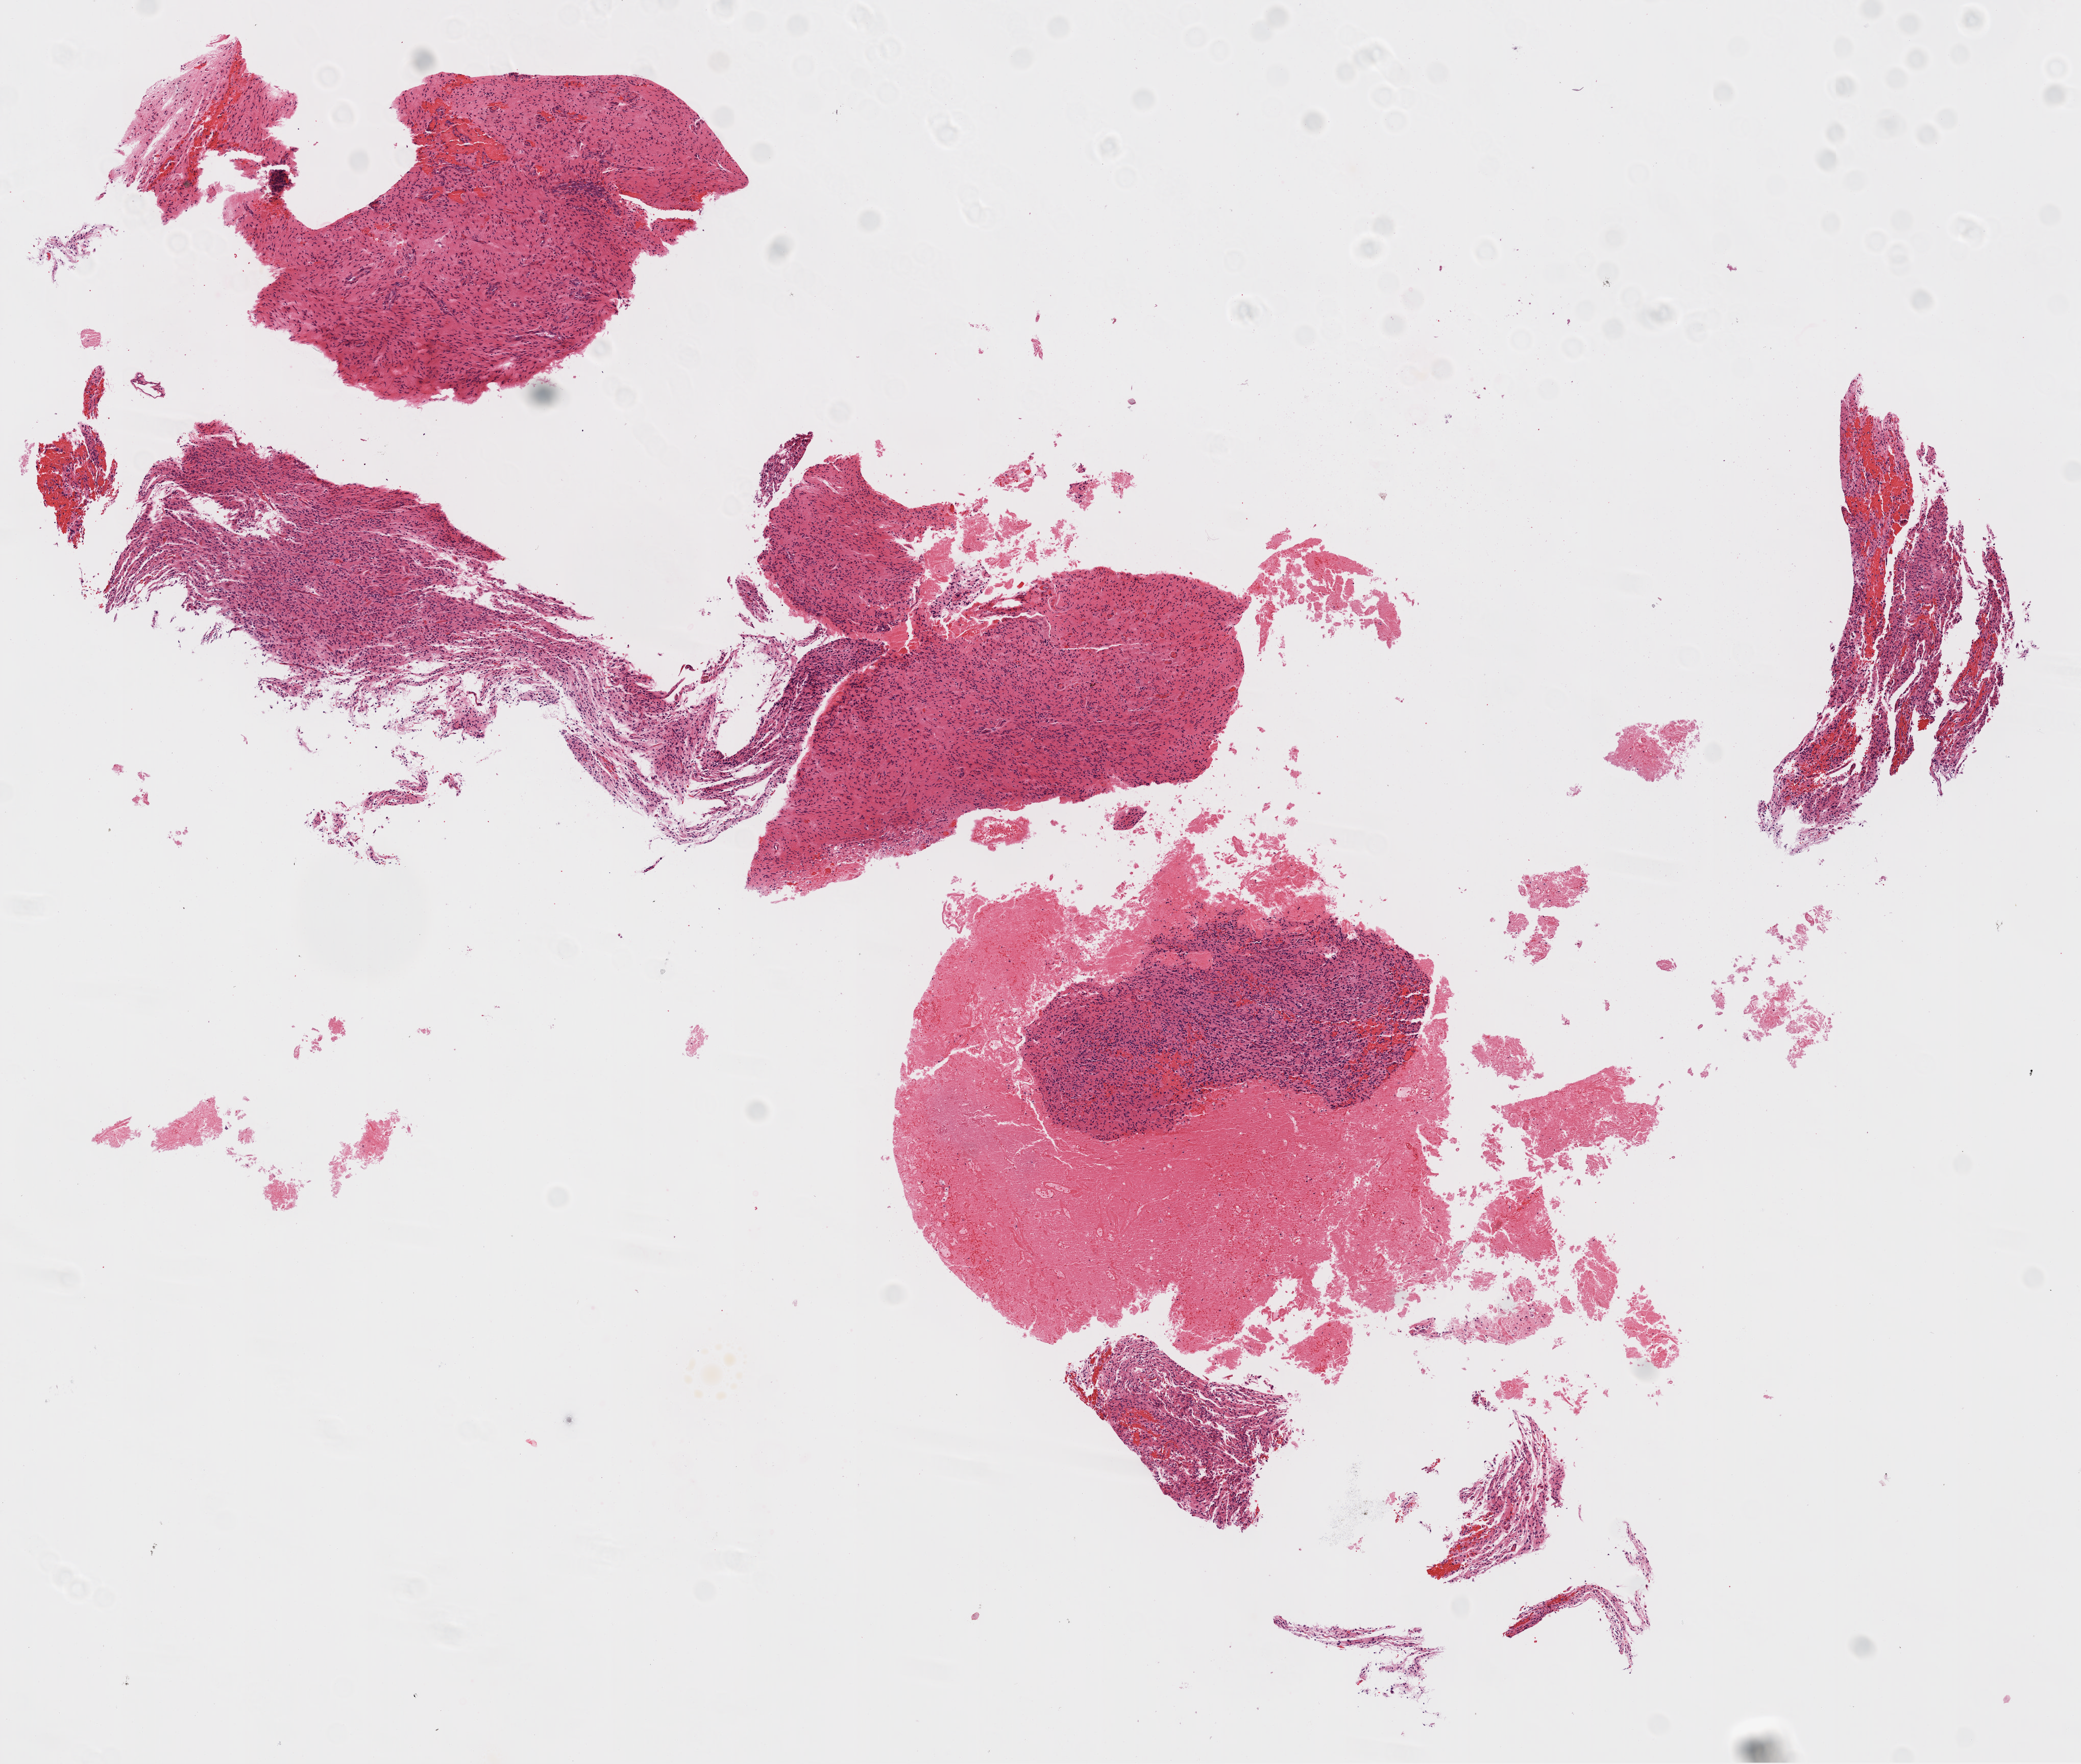
H&E whole-slide image — a low-resolution overview of the entire scanned area, about 8.2 x 7.0 mm (from a 20x scan), FFPE section, primary tumour sample from the brain. Female patient; age at initial diagnosis 63 years.
Diagnosis: Glioblastoma.